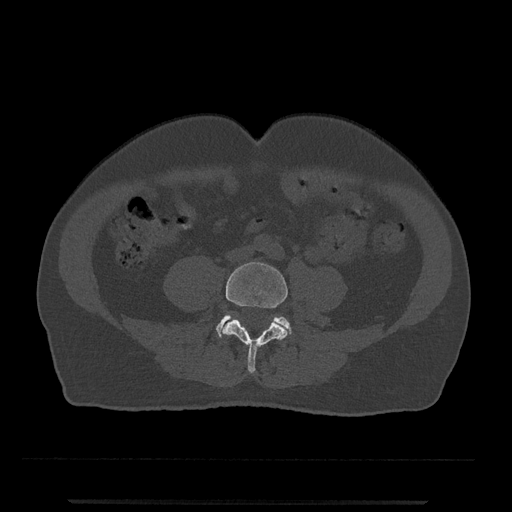
CT including the spine, one axial slice; position 118 of 797 along the scan axis; 120 kVp; bone window (W 1800 / L 400 HU); 0.5 mm slice thickness; 512 × 512 image matrix, field of view 419 × 419 mm. Male patient, age 63 years. From the clinical record (not read from this slice): primary cancer: prostate.
Outlined on this slice (semi-automatic segmentation, software-assisted and operator-edited):
- L4 vertebra: bounding box <222,262,288,374> (left, top, right, bottom; pixels)
- L5 vertebra: <216,315,291,338>